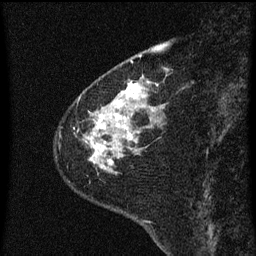
Breast MRI (dynamic contrast-enhanced), one sagittal slice; dynamic contrast-enhanced series, image 2 of 3 at this slice position (ordered by acquisition); 1.5 T; TE 4.2 ms, TR 8 ms; 2 mm slice thickness; 256 × 256 image matrix. Female patient, age 60 years.
Structures marked on this image (semi-automatically segmented with operator editing):
- analysis volume of interest (the breast-tissue region the enhancement analysis was run in; not a lesion): box from (x=62, y=82) to (x=159, y=175) px
- tumour enhancement mask (voxels above the 70 % enhancement threshold inside the analysis volume of interest): (x=94, y=84)–(x=141, y=155)